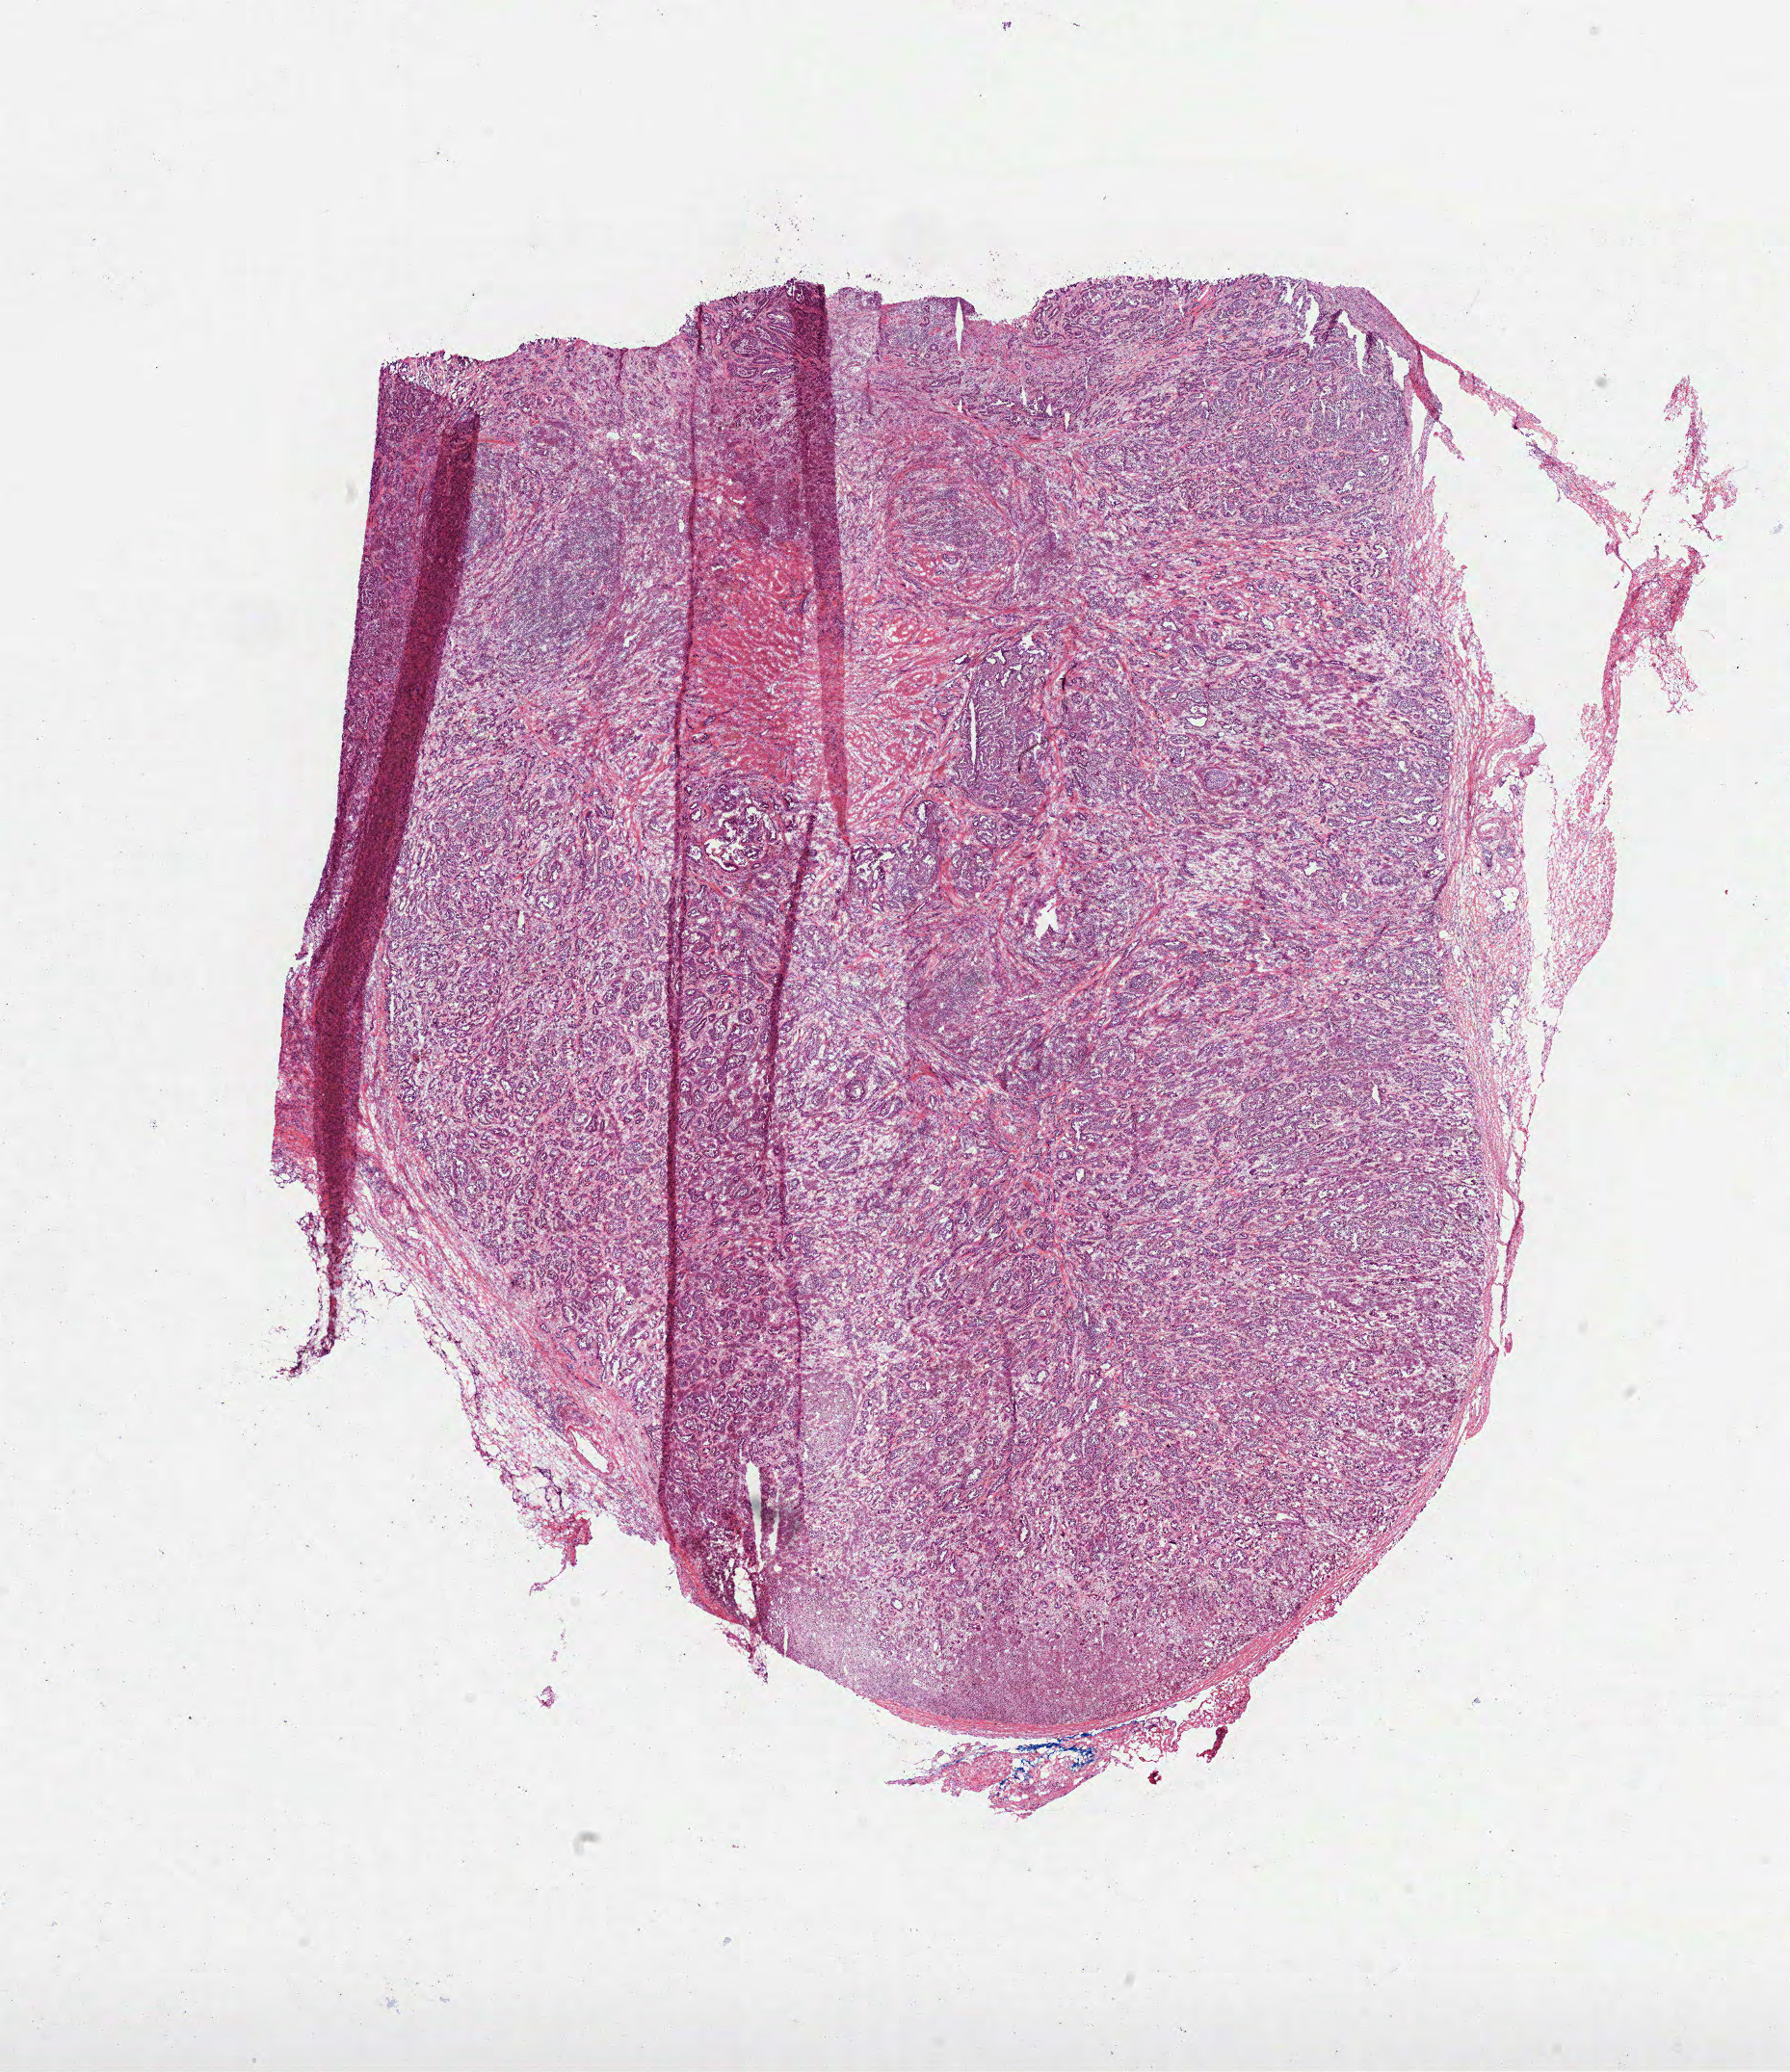
Whole-slide histology image, H&E — low-resolution overview of the scanned area, about 15.0 x 17.4 mm (slide scanned at 40x); frozen section from the top of the tissue portion; lung, recurrent tumour sample. Male, age 72 years at initial diagnosis. Pathologist review of this section (percent, as recorded): tumour cells 81%, tumour nuclei 65%, normal cells 0%, stromal cells 19%, necrosis 0%. Inflammatory infiltration, as recorded: lymphocyte infiltration 15%, monocyte infiltration 5%, neutrophil infiltration 0%.
This section: recurrent tumour. Patient diagnosis: Adenocarcinoma with mixed subtypes (upper lobe, lung).